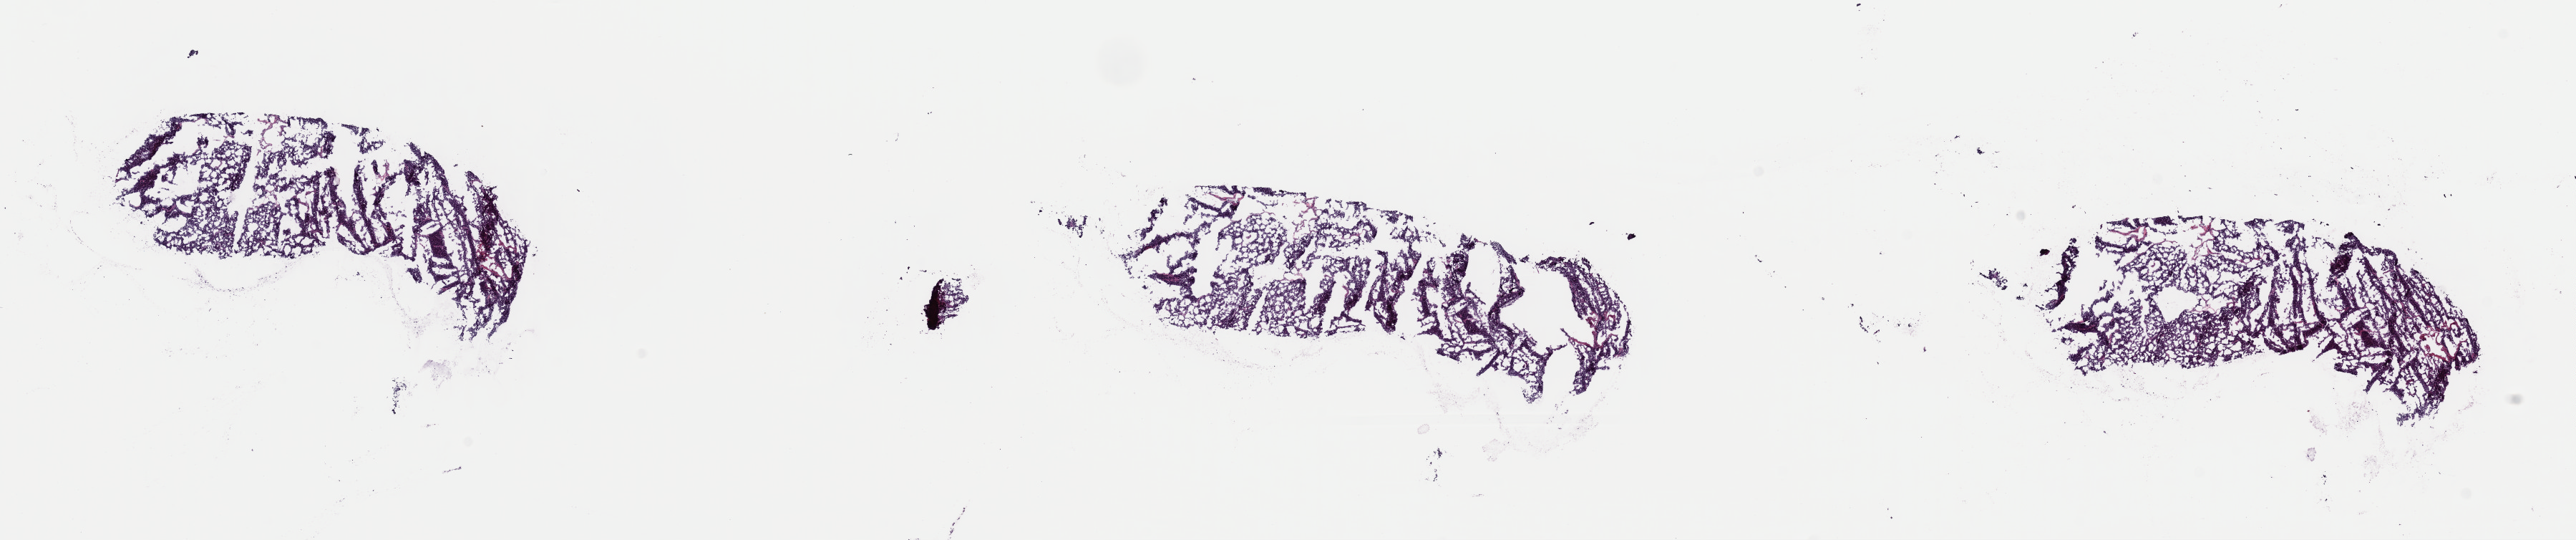
Digitized H&E tissue section (whole slide), low-resolution overview of the scanned area, about 28.4 x 6.0 mm (from a 40x scan), frozen section from the top of the tissue portion, adrenal gland, primary tumour sample. Male, age 56 years at initial diagnosis. Pathologist review of this section (percent, as recorded): tumour cells 100%, tumour nuclei 80%, normal cells 0%, stromal cells 0%, necrosis 0%. Inflammatory infiltration, as recorded: lymphocyte infiltration 1%, monocyte infiltration 0%, neutrophil infiltration 0%.
Laterality: right. Diagnosis: Pheochromocytoma, NOS.